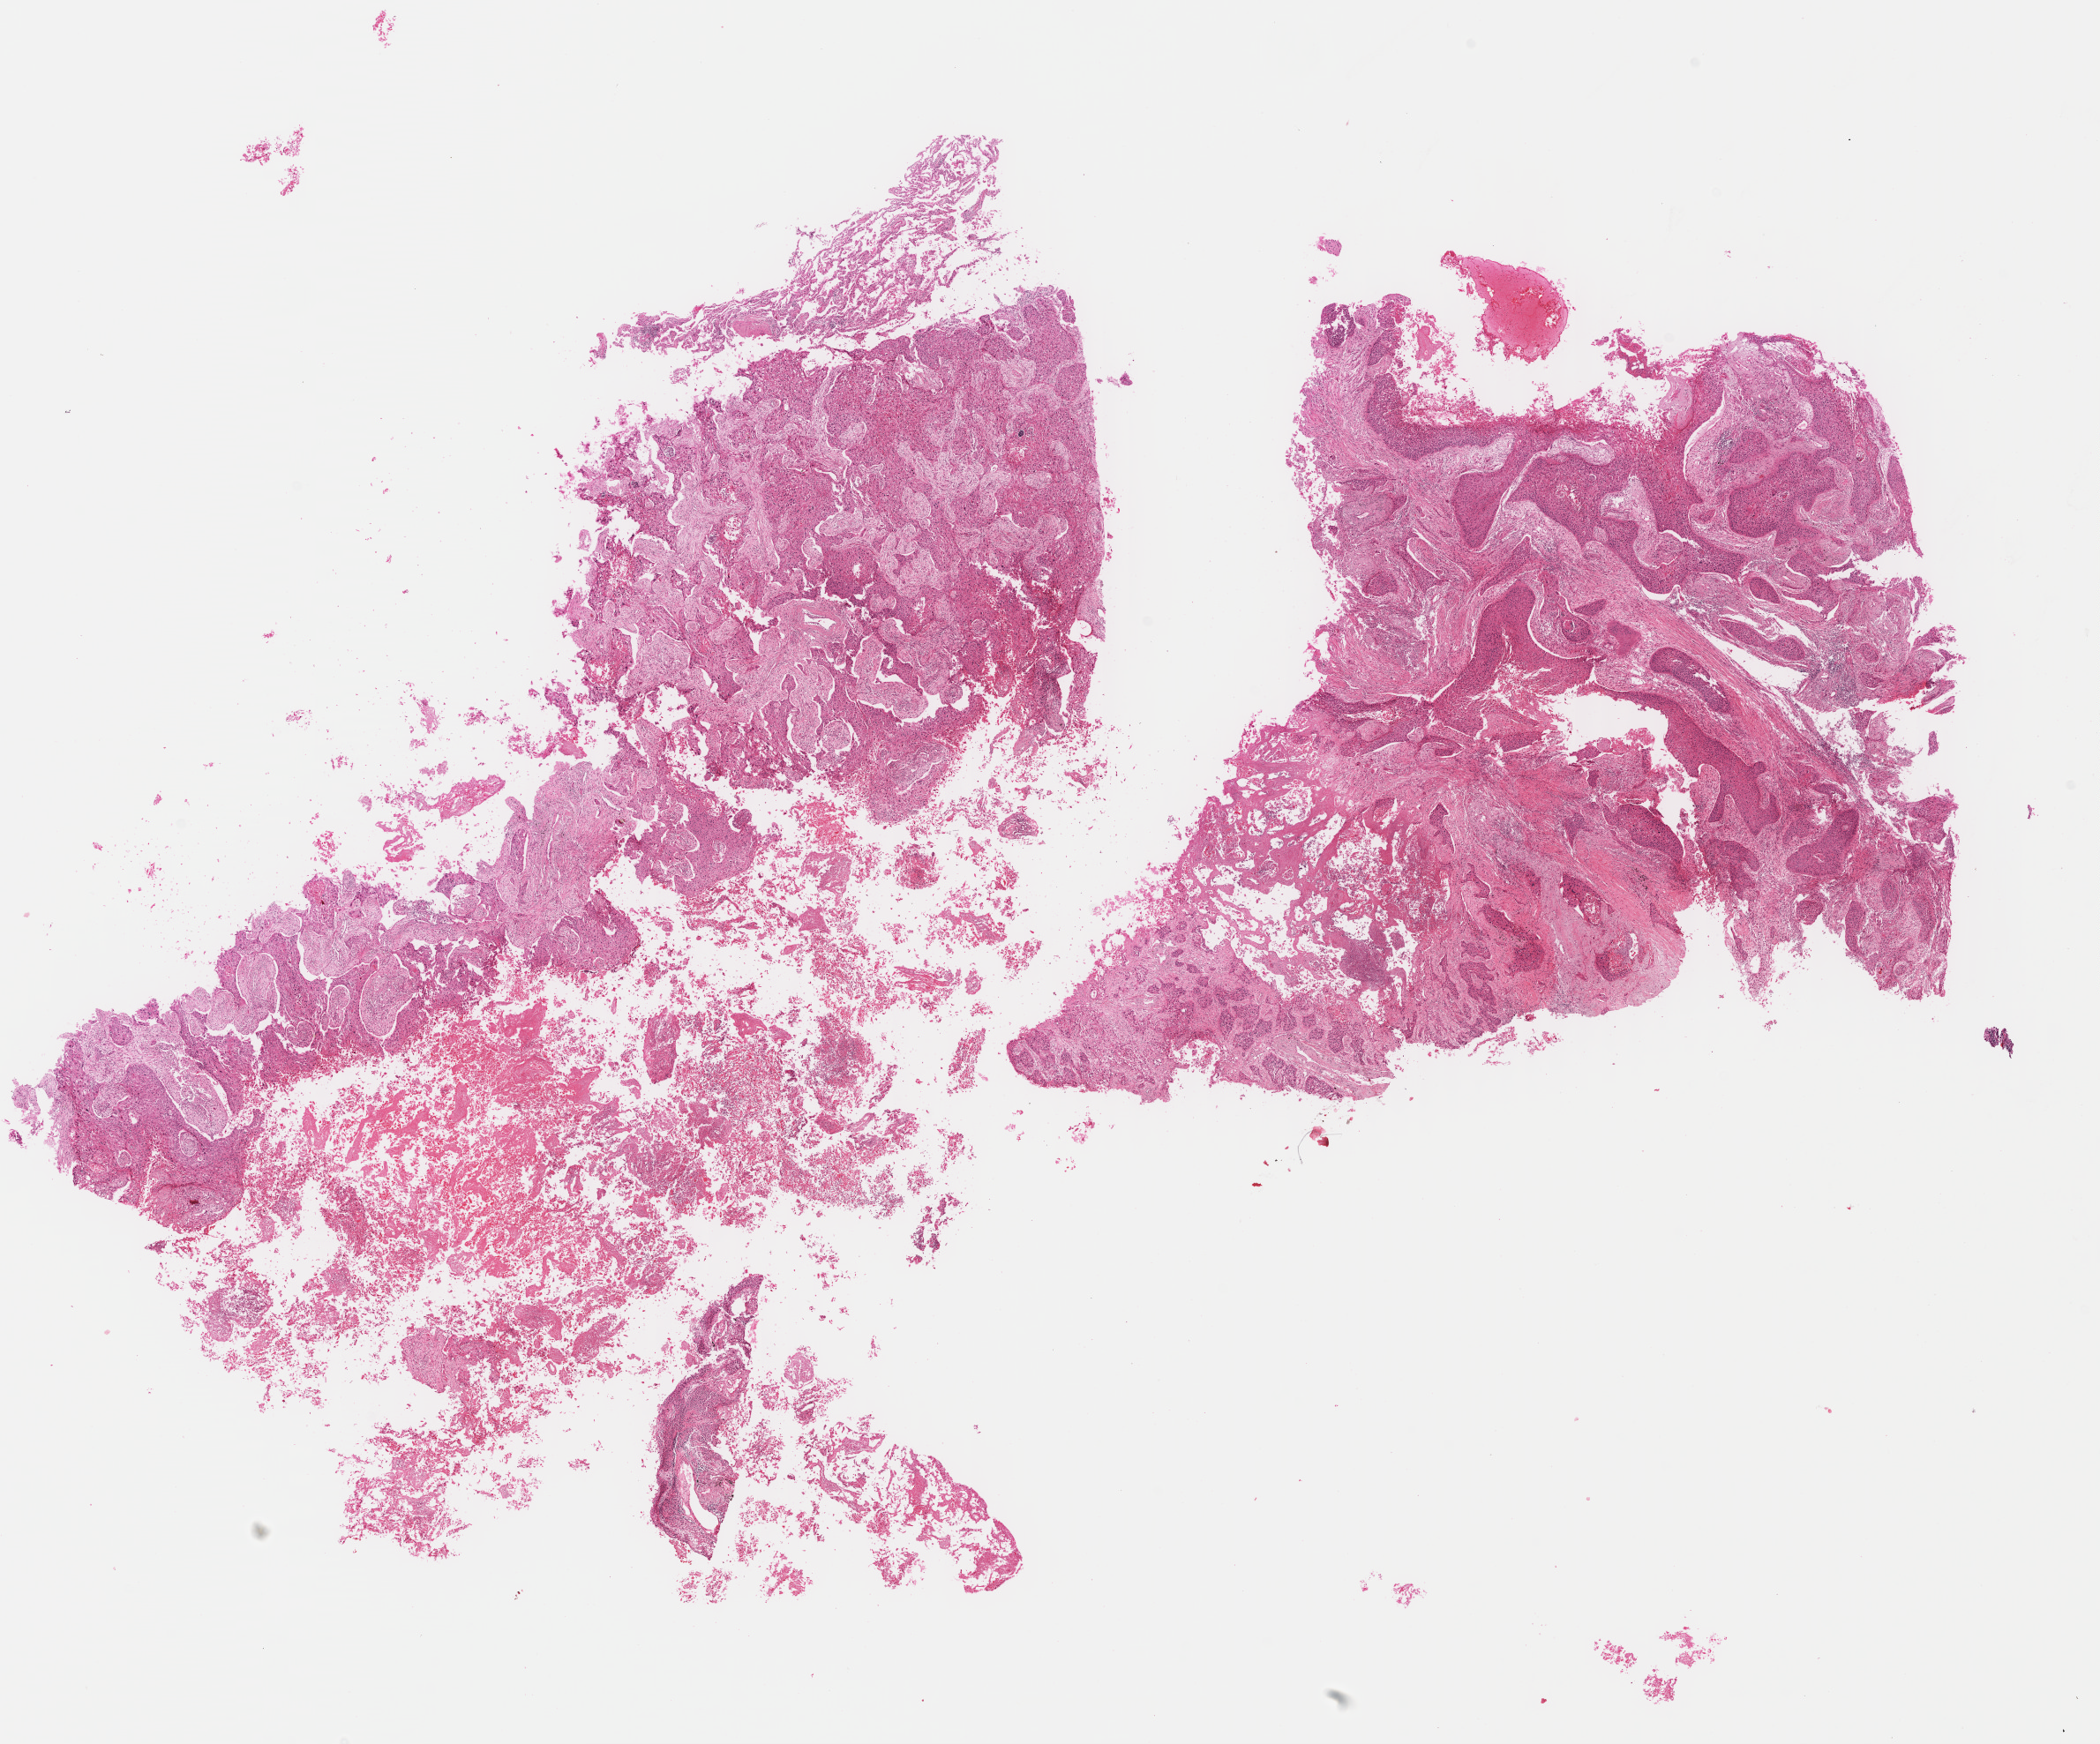
Digitized Hematoxylin and eosin (H&E) stained tissue section (whole slide), shown as a low-resolution overview of the whole scanned area (about 18.7 x 15.5 mm, from a 40x scan); FFPE section; sample: primary tumour, lung. Male, age 77 years at initial diagnosis.
• TNM: T1b N0 M0
• diagnosis: Squamous cell carcinoma, NOS (lower lobe, lung)
• AJCC pathologic stage: IA (6th edition)